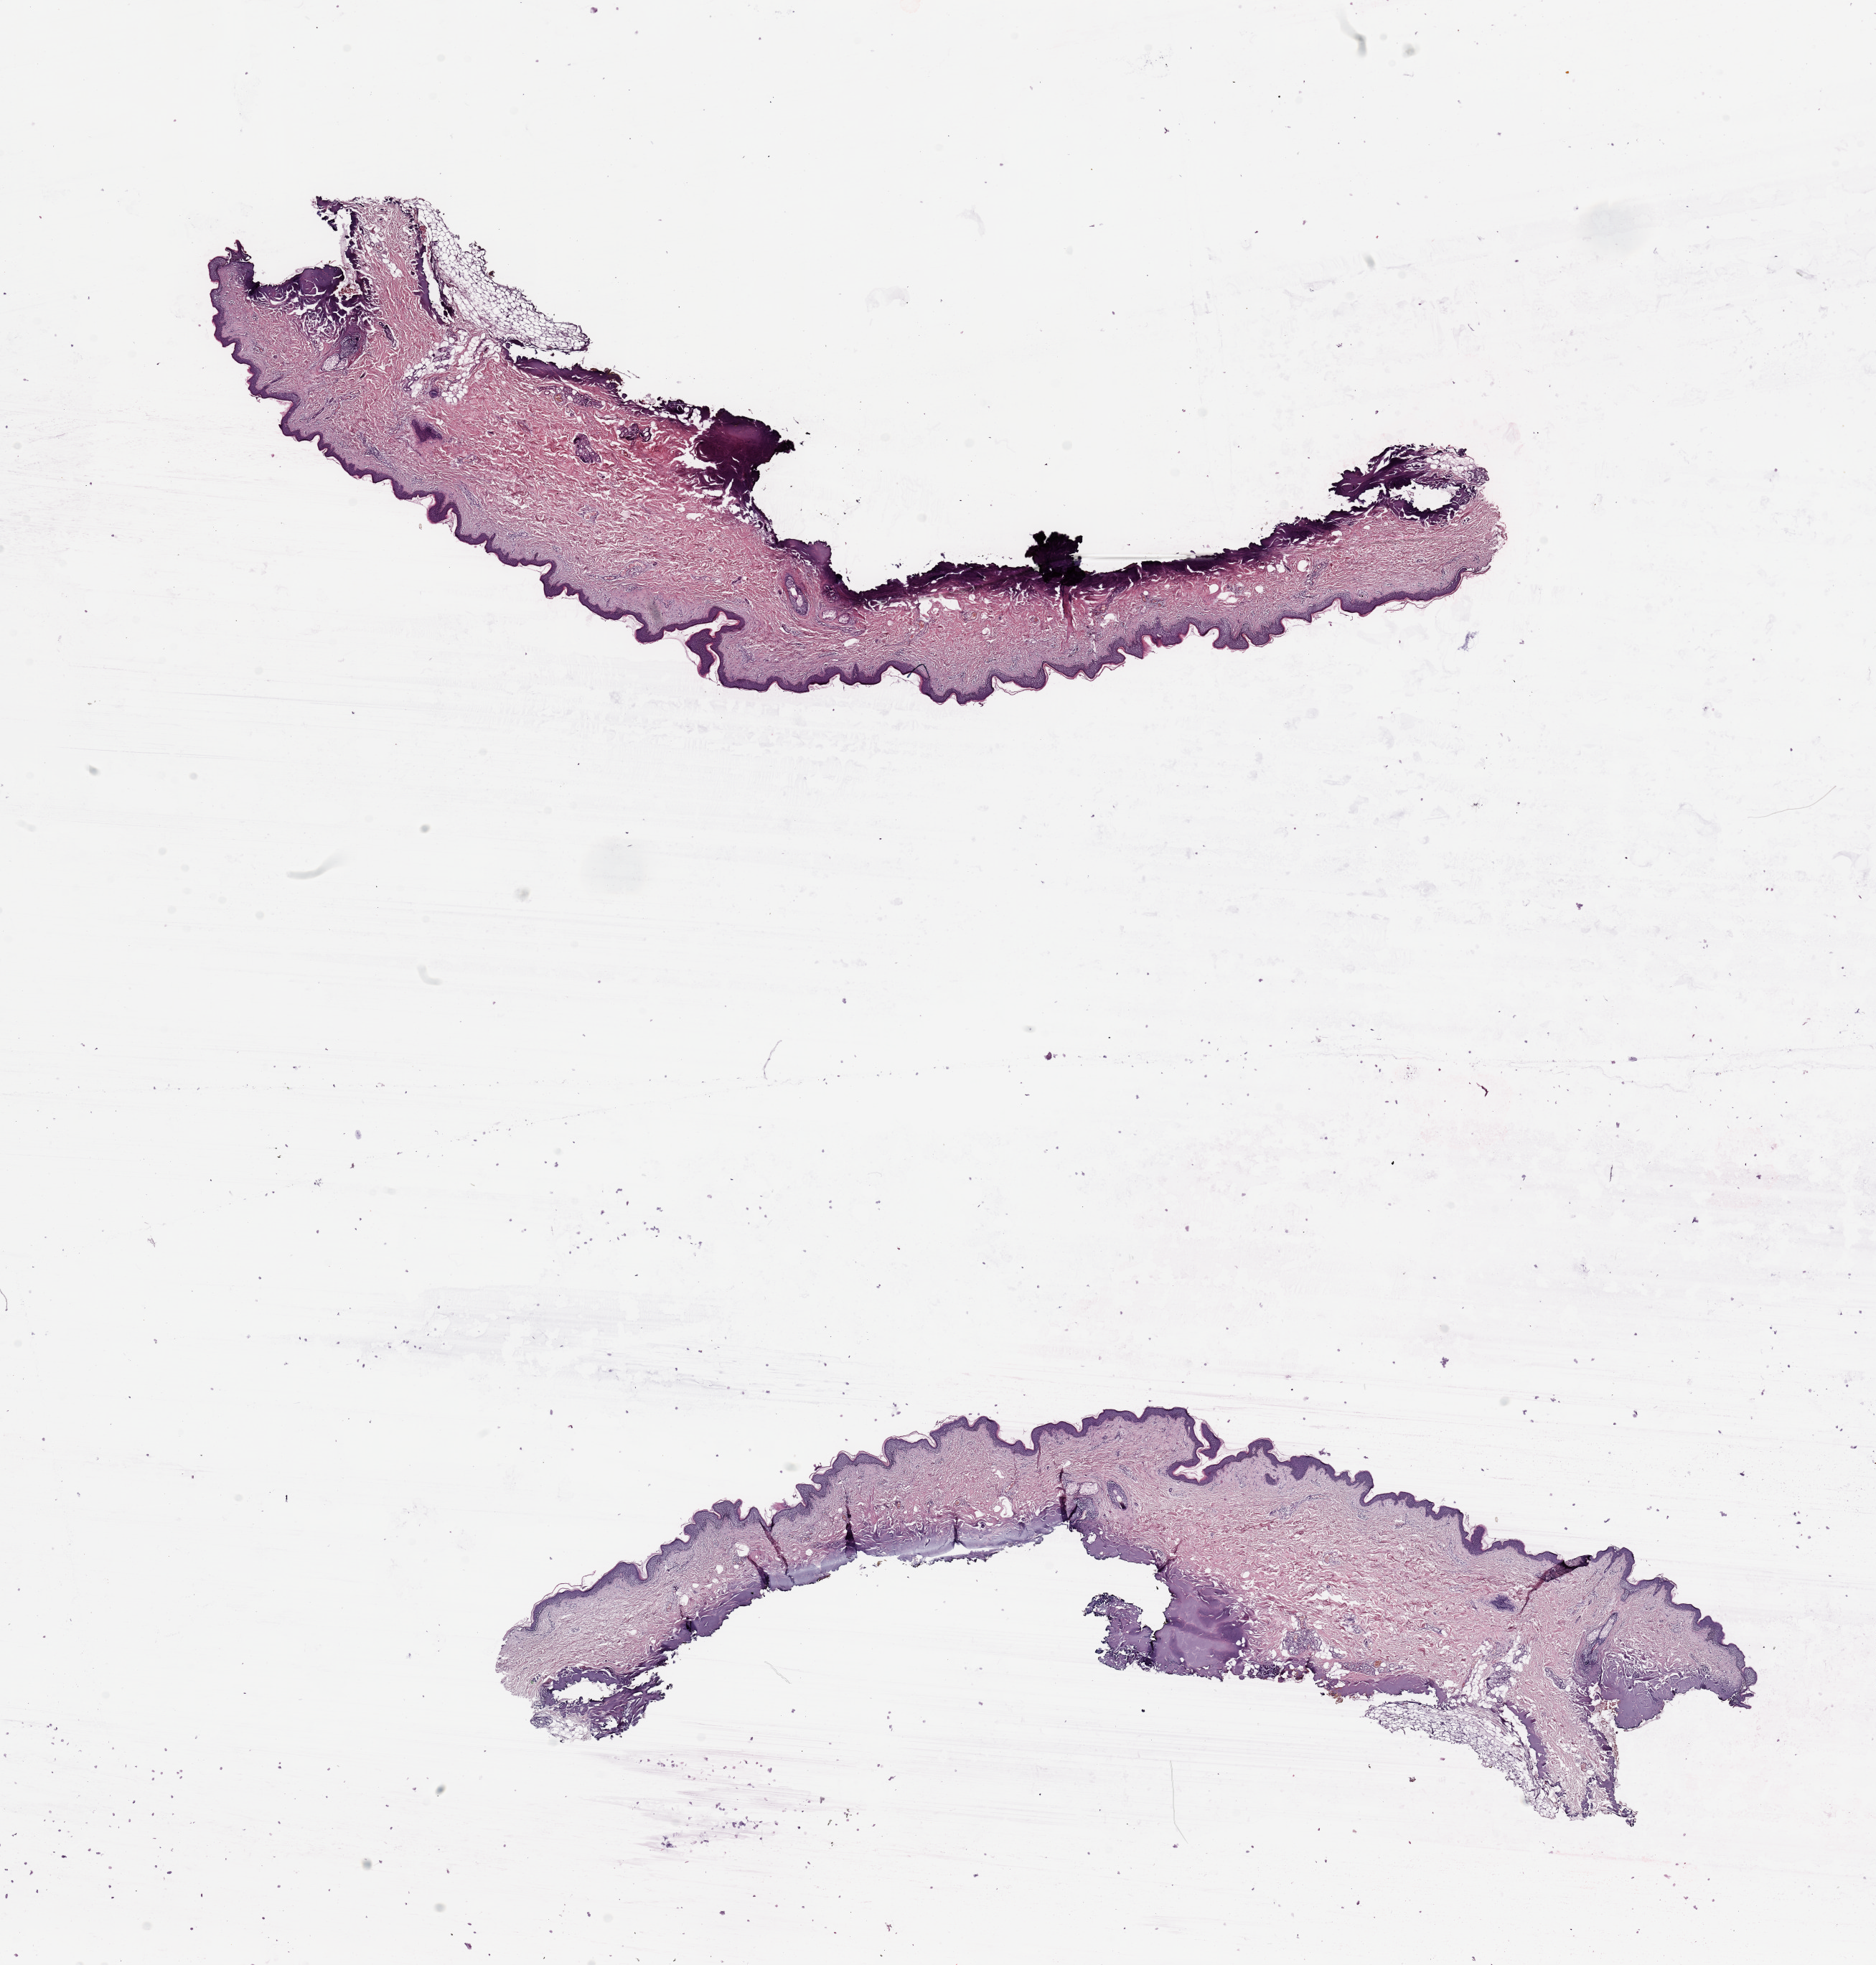
Whole-slide histology image, Hematoxylin and eosin (H&E) stained — whole scanned area (about 20.7 x 21.7 mm, from a 20x scan) shown as a low-resolution overview; normal (non-tumour) tissue sample, sampled site: trunk. Patient: male, age 45 years.
* this section: normal (non-tumour) tissue from the same patient
* patient diagnosis: Malignant melanoma, NOS